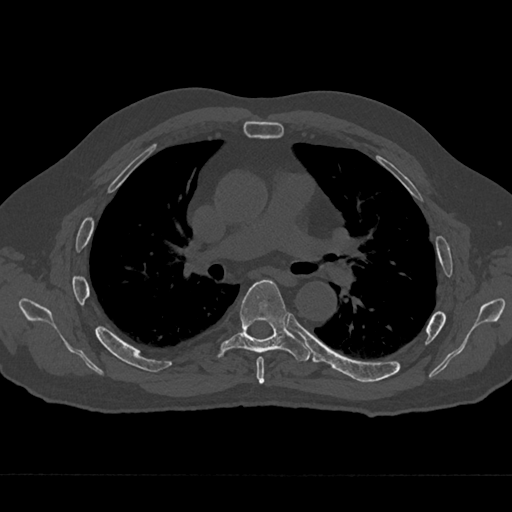
CT including the spine, one axial slice. Reconstruction kernel Br40s/3. 120 kVp. Bone window (W 1800 / L 400 HU). 0.5 mm slice thickness. 512 × 512 image matrix, field of view 377 × 377 mm. Male patient, age 75 years. From the clinical record (not read from this slice): primary cancer: renal; vertebrae with lytic lesions (as recorded): T4.
Annotated regions visible in this slice (semi-automatic segmentation, software-assisted and operator-edited):
- T5 vertebra: bounding box (x1, y1, x2, y2) in pixels: (256, 356, 265, 384)
- T6 vertebra: (217, 279, 310, 362)